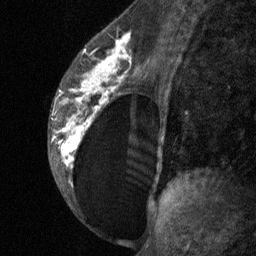
Breast MRI (dynamic contrast-enhanced), one sagittal slice; position 38 of 64 along the scan axis; dynamic contrast-enhanced study with each time point stored as its own series, time point 2 of 3 at this slice position (early post-contrast, ordered by acquisition time); 1.5 T; TE 4.8 ms, TR 27 ms; 256 × 256 image matrix, field of view 180 × 180 mm. Female patient, age 34 years. Case-level facts recorded for this patient, not image findings: setting: breast cancer imaged before/during neoadjuvant chemotherapy; receptor status: HR-positive, HER2-negative.
Structures marked on this image (semi-automatically segmented with operator editing):
- analysis volume of interest (the breast-tissue region the enhancement analysis was run in; not a lesion): bounding box <47,23,157,197> (left, top, right, bottom; pixels)
- tumour enhancement mask (voxels above the 90 % enhancement threshold inside the analysis volume of interest): <53,33,131,168>